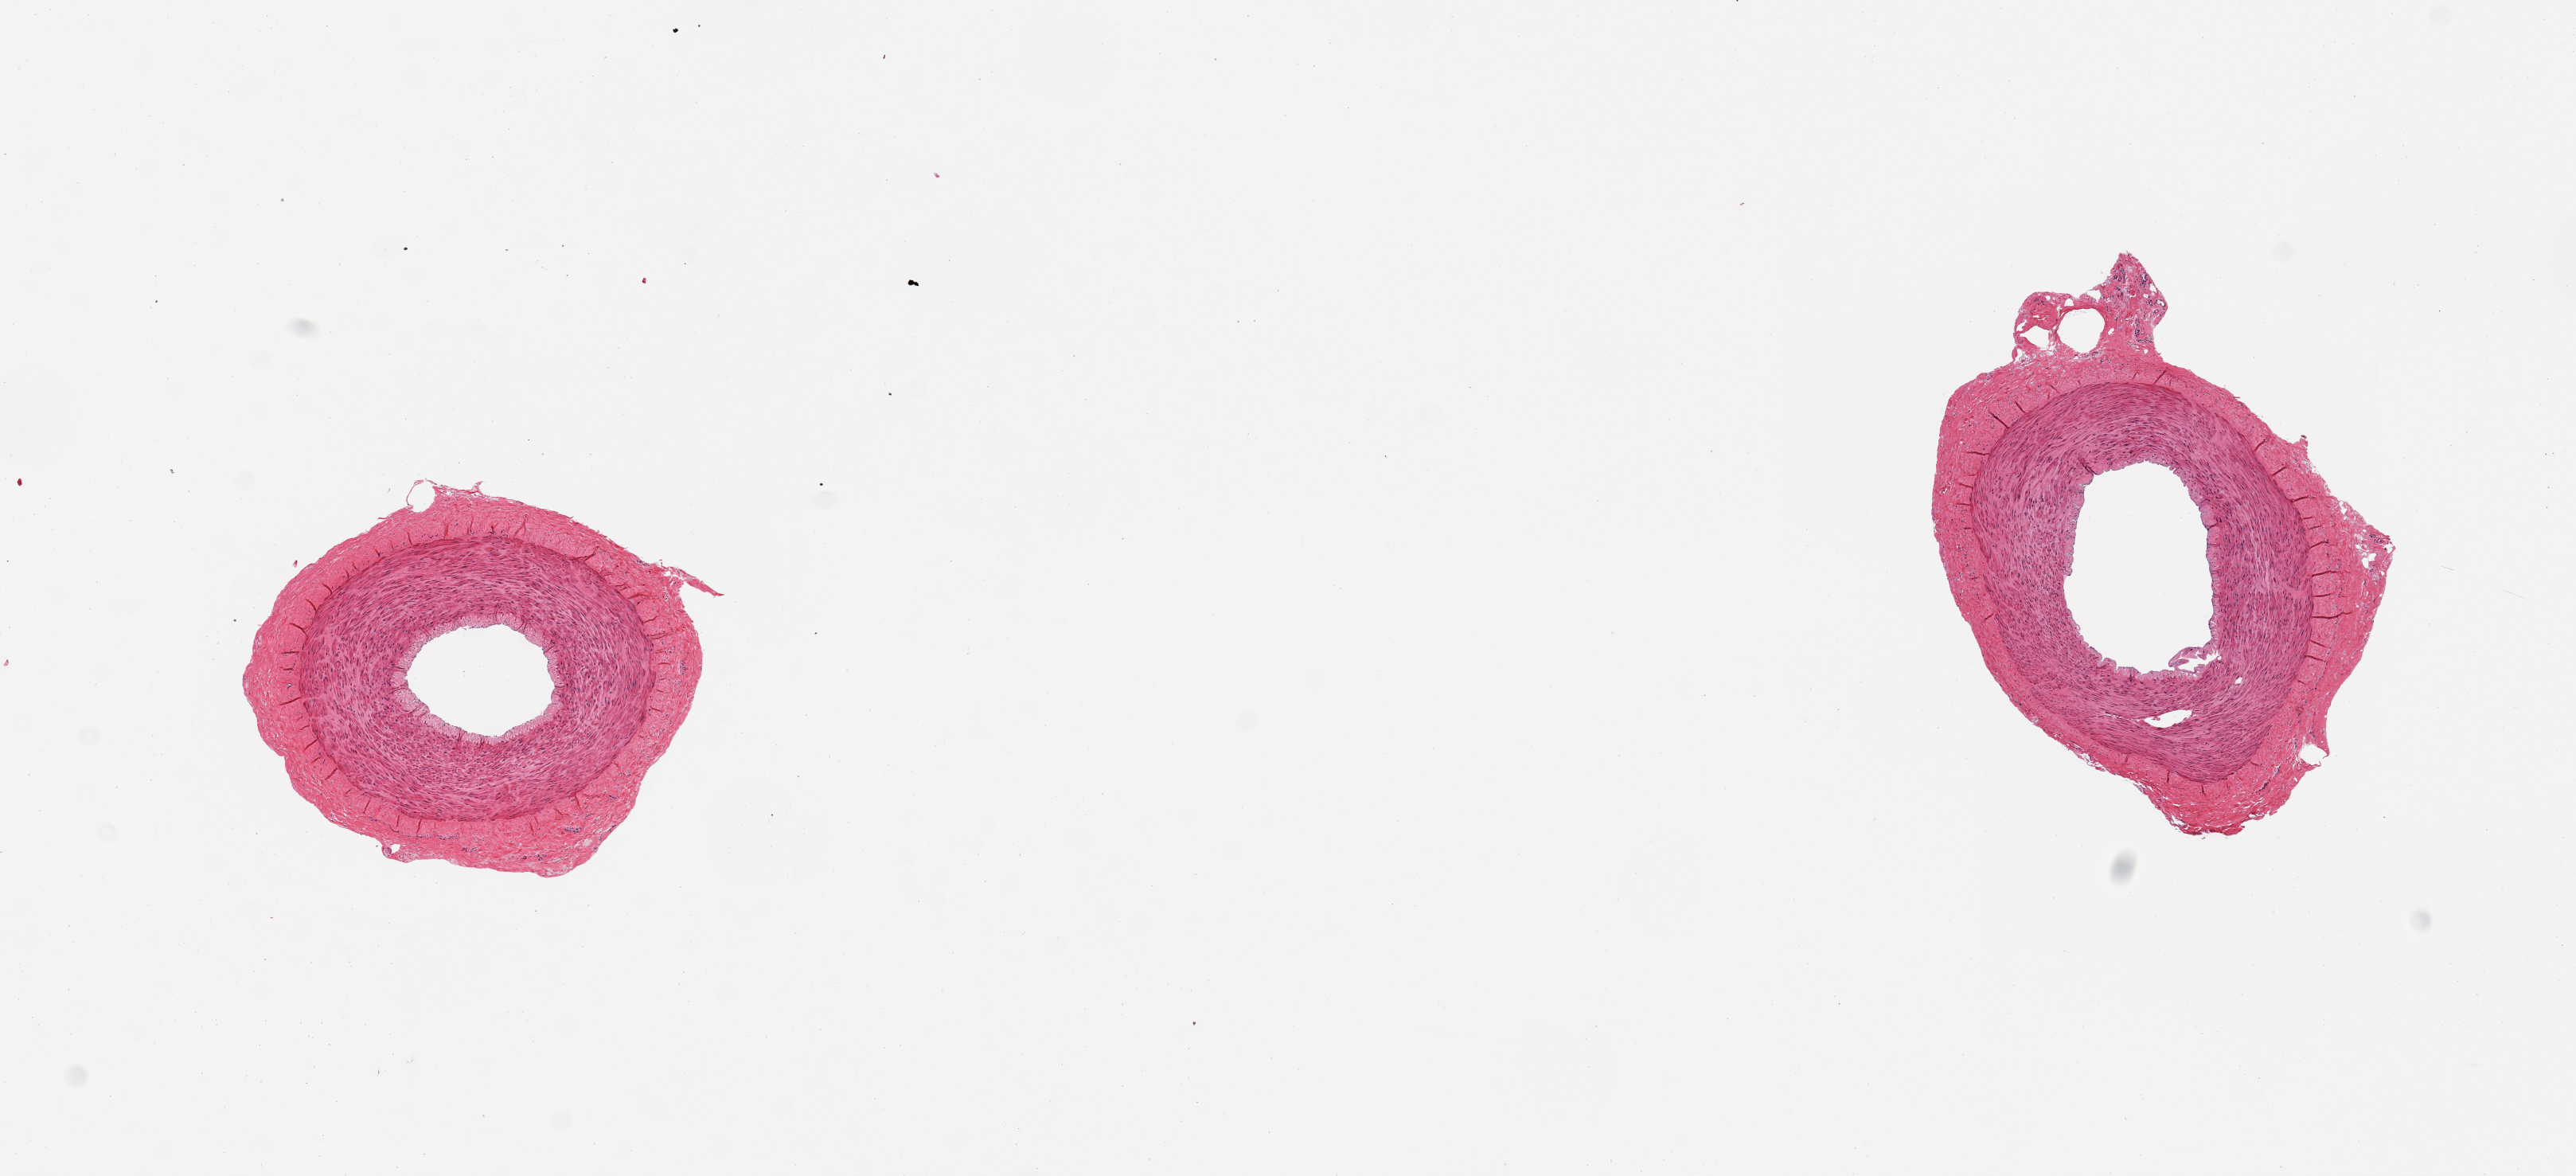
Whole-slide image, haematoxylin and eosin stain — shown as a low-resolution overview of the whole scanned area (about 12.8 x 5.8 mm, acquisition: 20x scan), PAXgene-fixed, paraffin-embedded tissue, target tissue: tibial artery, donor tissue sample. Donor: male.
Review note (as recorded): 2 pieces, 2x2 & 3x2mm; good clean aliquots.